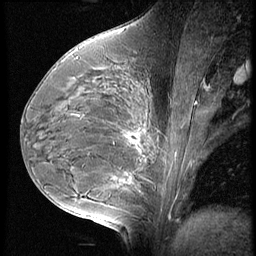
Breast MRI (dynamic contrast-enhanced), one sagittal slice. Position 31 of 60 along the scan axis. 3 images stored at this slice position (order not interpretable as contrast timing). 1.5 T. TE 4.2 ms, TR 9 ms. 2.5 mm slice thickness. 256 × 256 image matrix. Patient: female, 35 years. Case-level facts recorded for this patient, not image findings: setting: breast cancer imaged before/during neoadjuvant chemotherapy; receptor status: HR-positive, HER2-negative.
Outlined on this slice (semi-automatic segmentation, software-assisted and operator-edited):
- analysis volume of interest (the breast-tissue region the enhancement analysis was run in; not a lesion): box from (x=56, y=58) to (x=176, y=202) px
- tumour enhancement mask (voxels above the 140 % enhancement threshold inside the analysis volume of interest): (x=115, y=134)–(x=141, y=183)